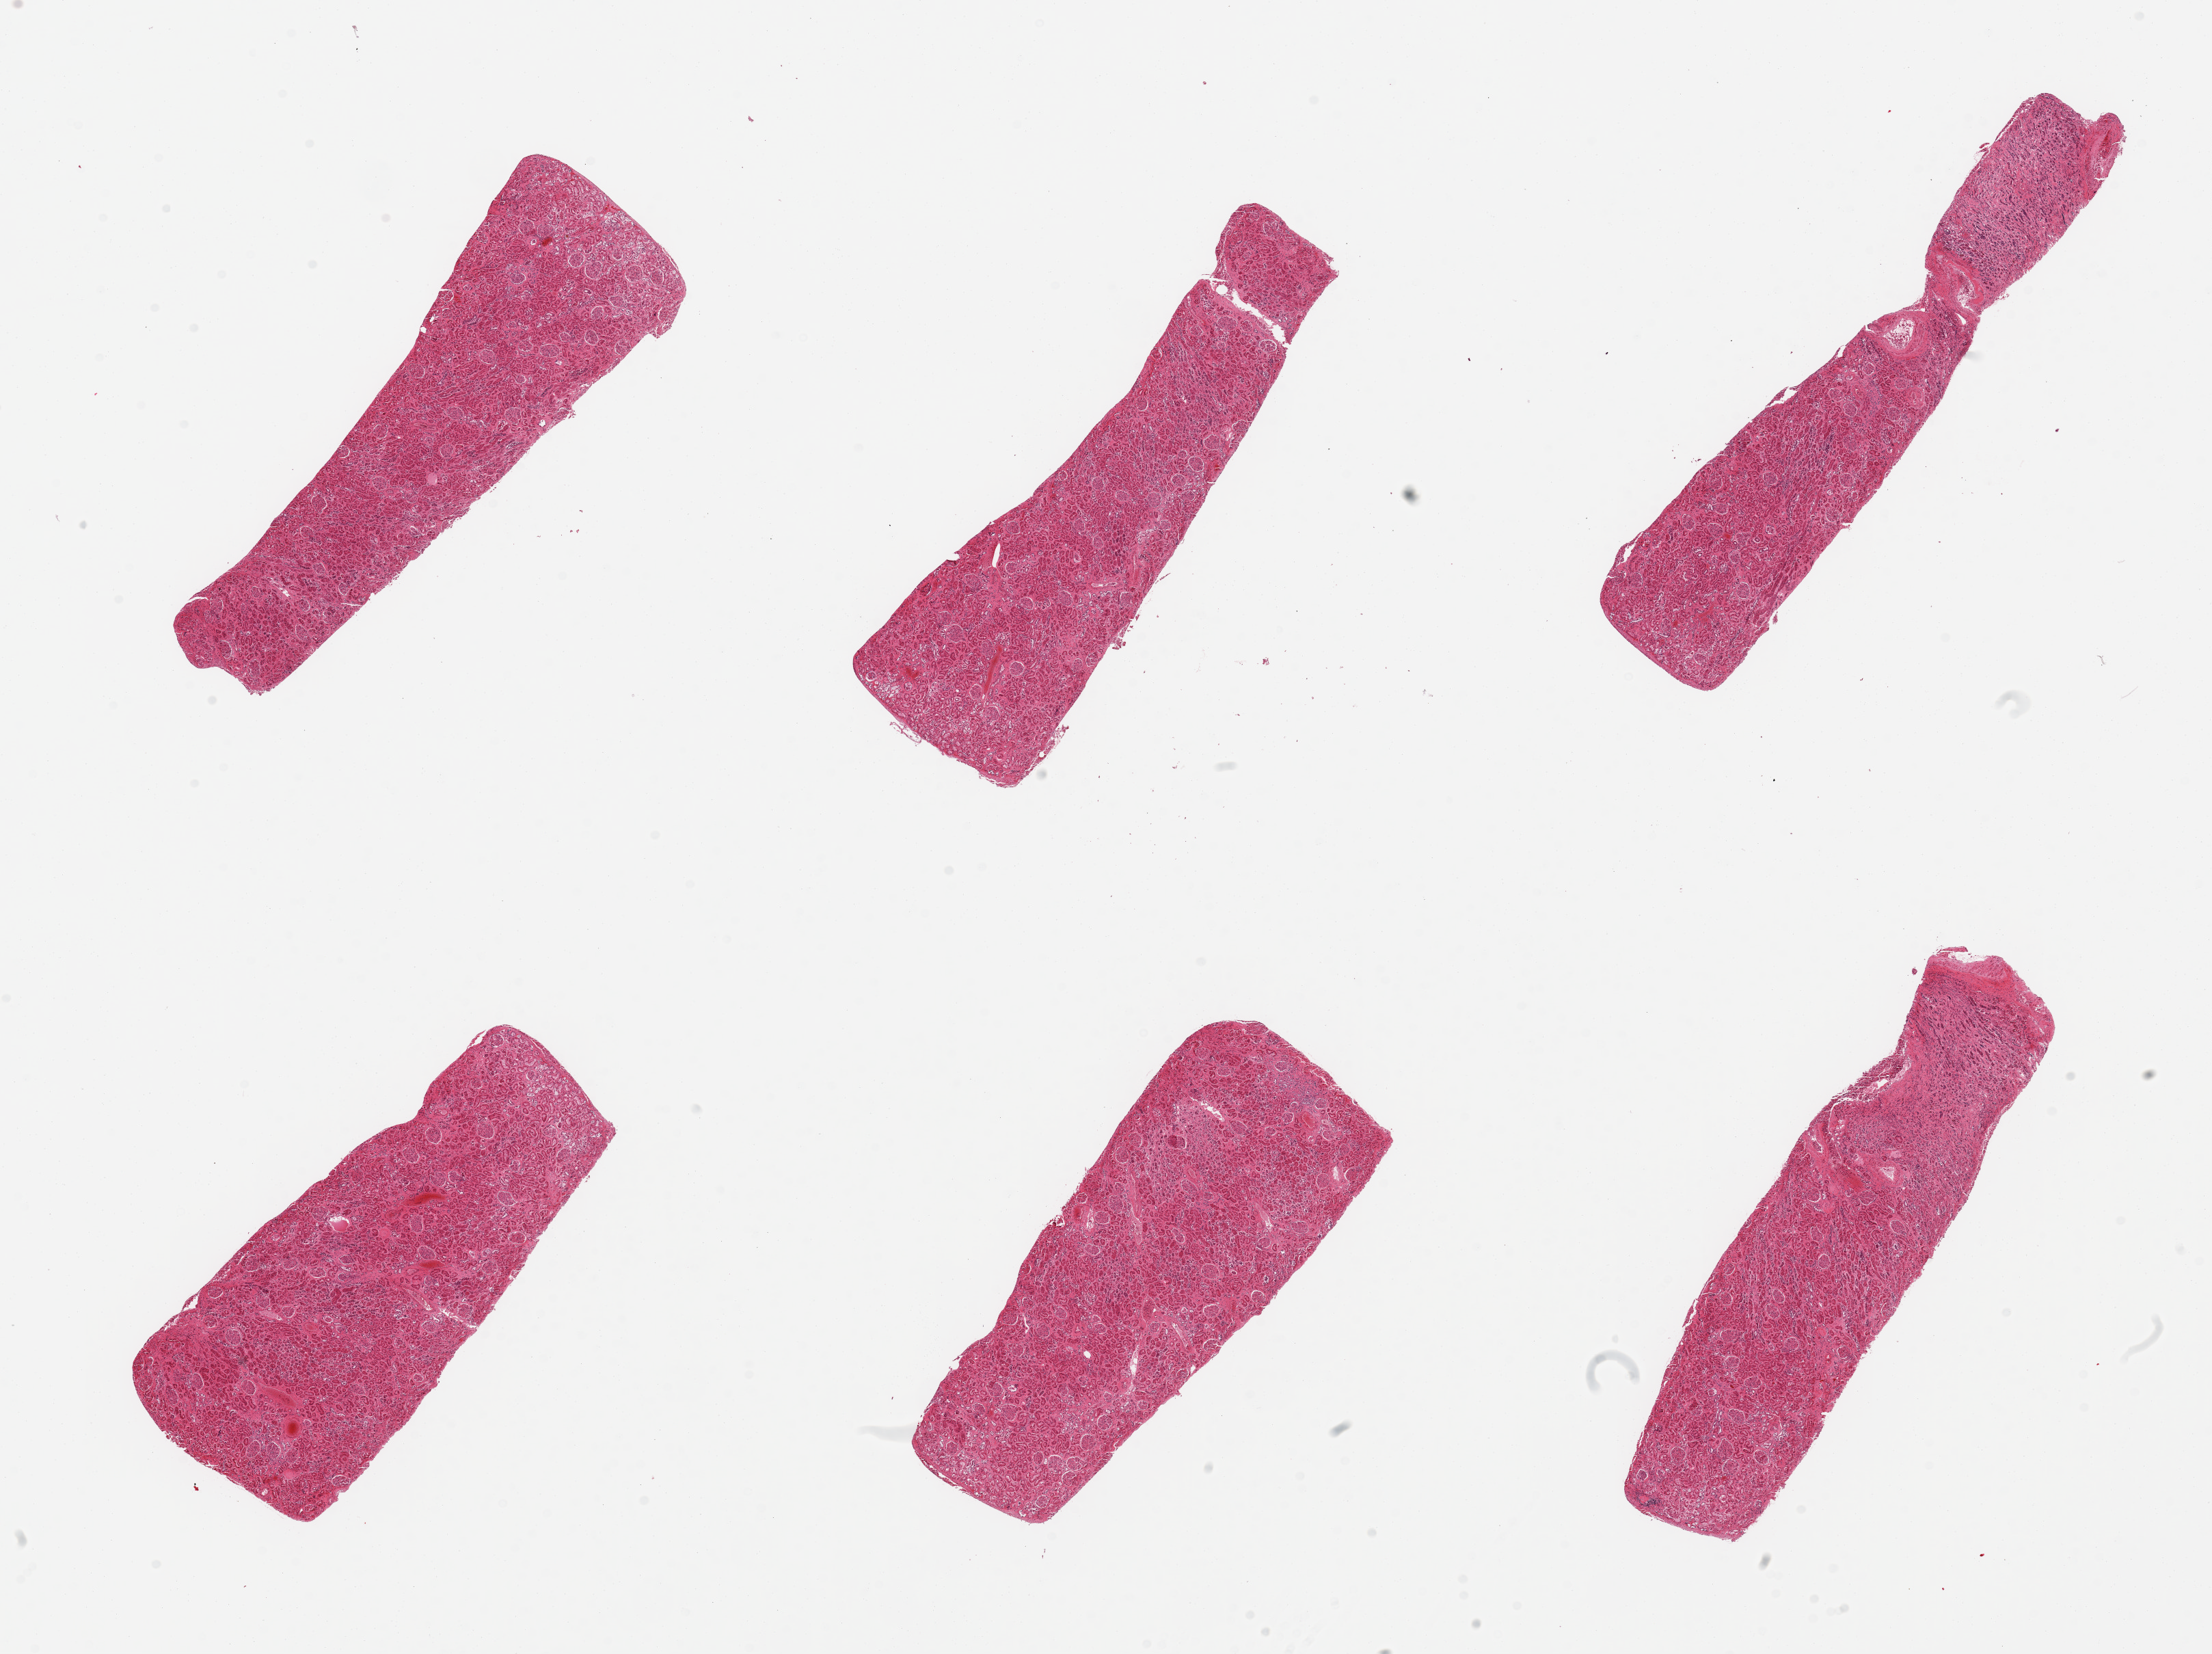
Digitized haematoxylin and eosin-stained section, low-resolution overview of the scanned area, about 25.6 x 19.1 mm (acquisition: 20x scan). Donor: male.
Specimen: PAXgene-fixed, paraffin-embedded tissue; sampled site (target tissue): renal cortex; tissue donor sample.